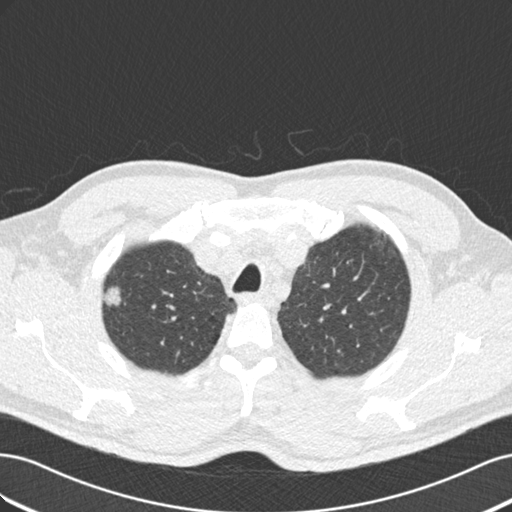
Low-dose screening chest CT, one axial slice; position 150 of 187 along the scan axis; reconstruction kernel B30f; 120 kVp; lung window (W 1500 / L -600 HU); 2 mm slice thickness; 512 × 512 image matrix.
Annotated regions visible in this slice (manually delineated by an expert):
- lesion 1 (tumor, upper lobe of right lung): bounding box (x1, y1, x2, y2) in pixels: (103, 287, 121, 306)